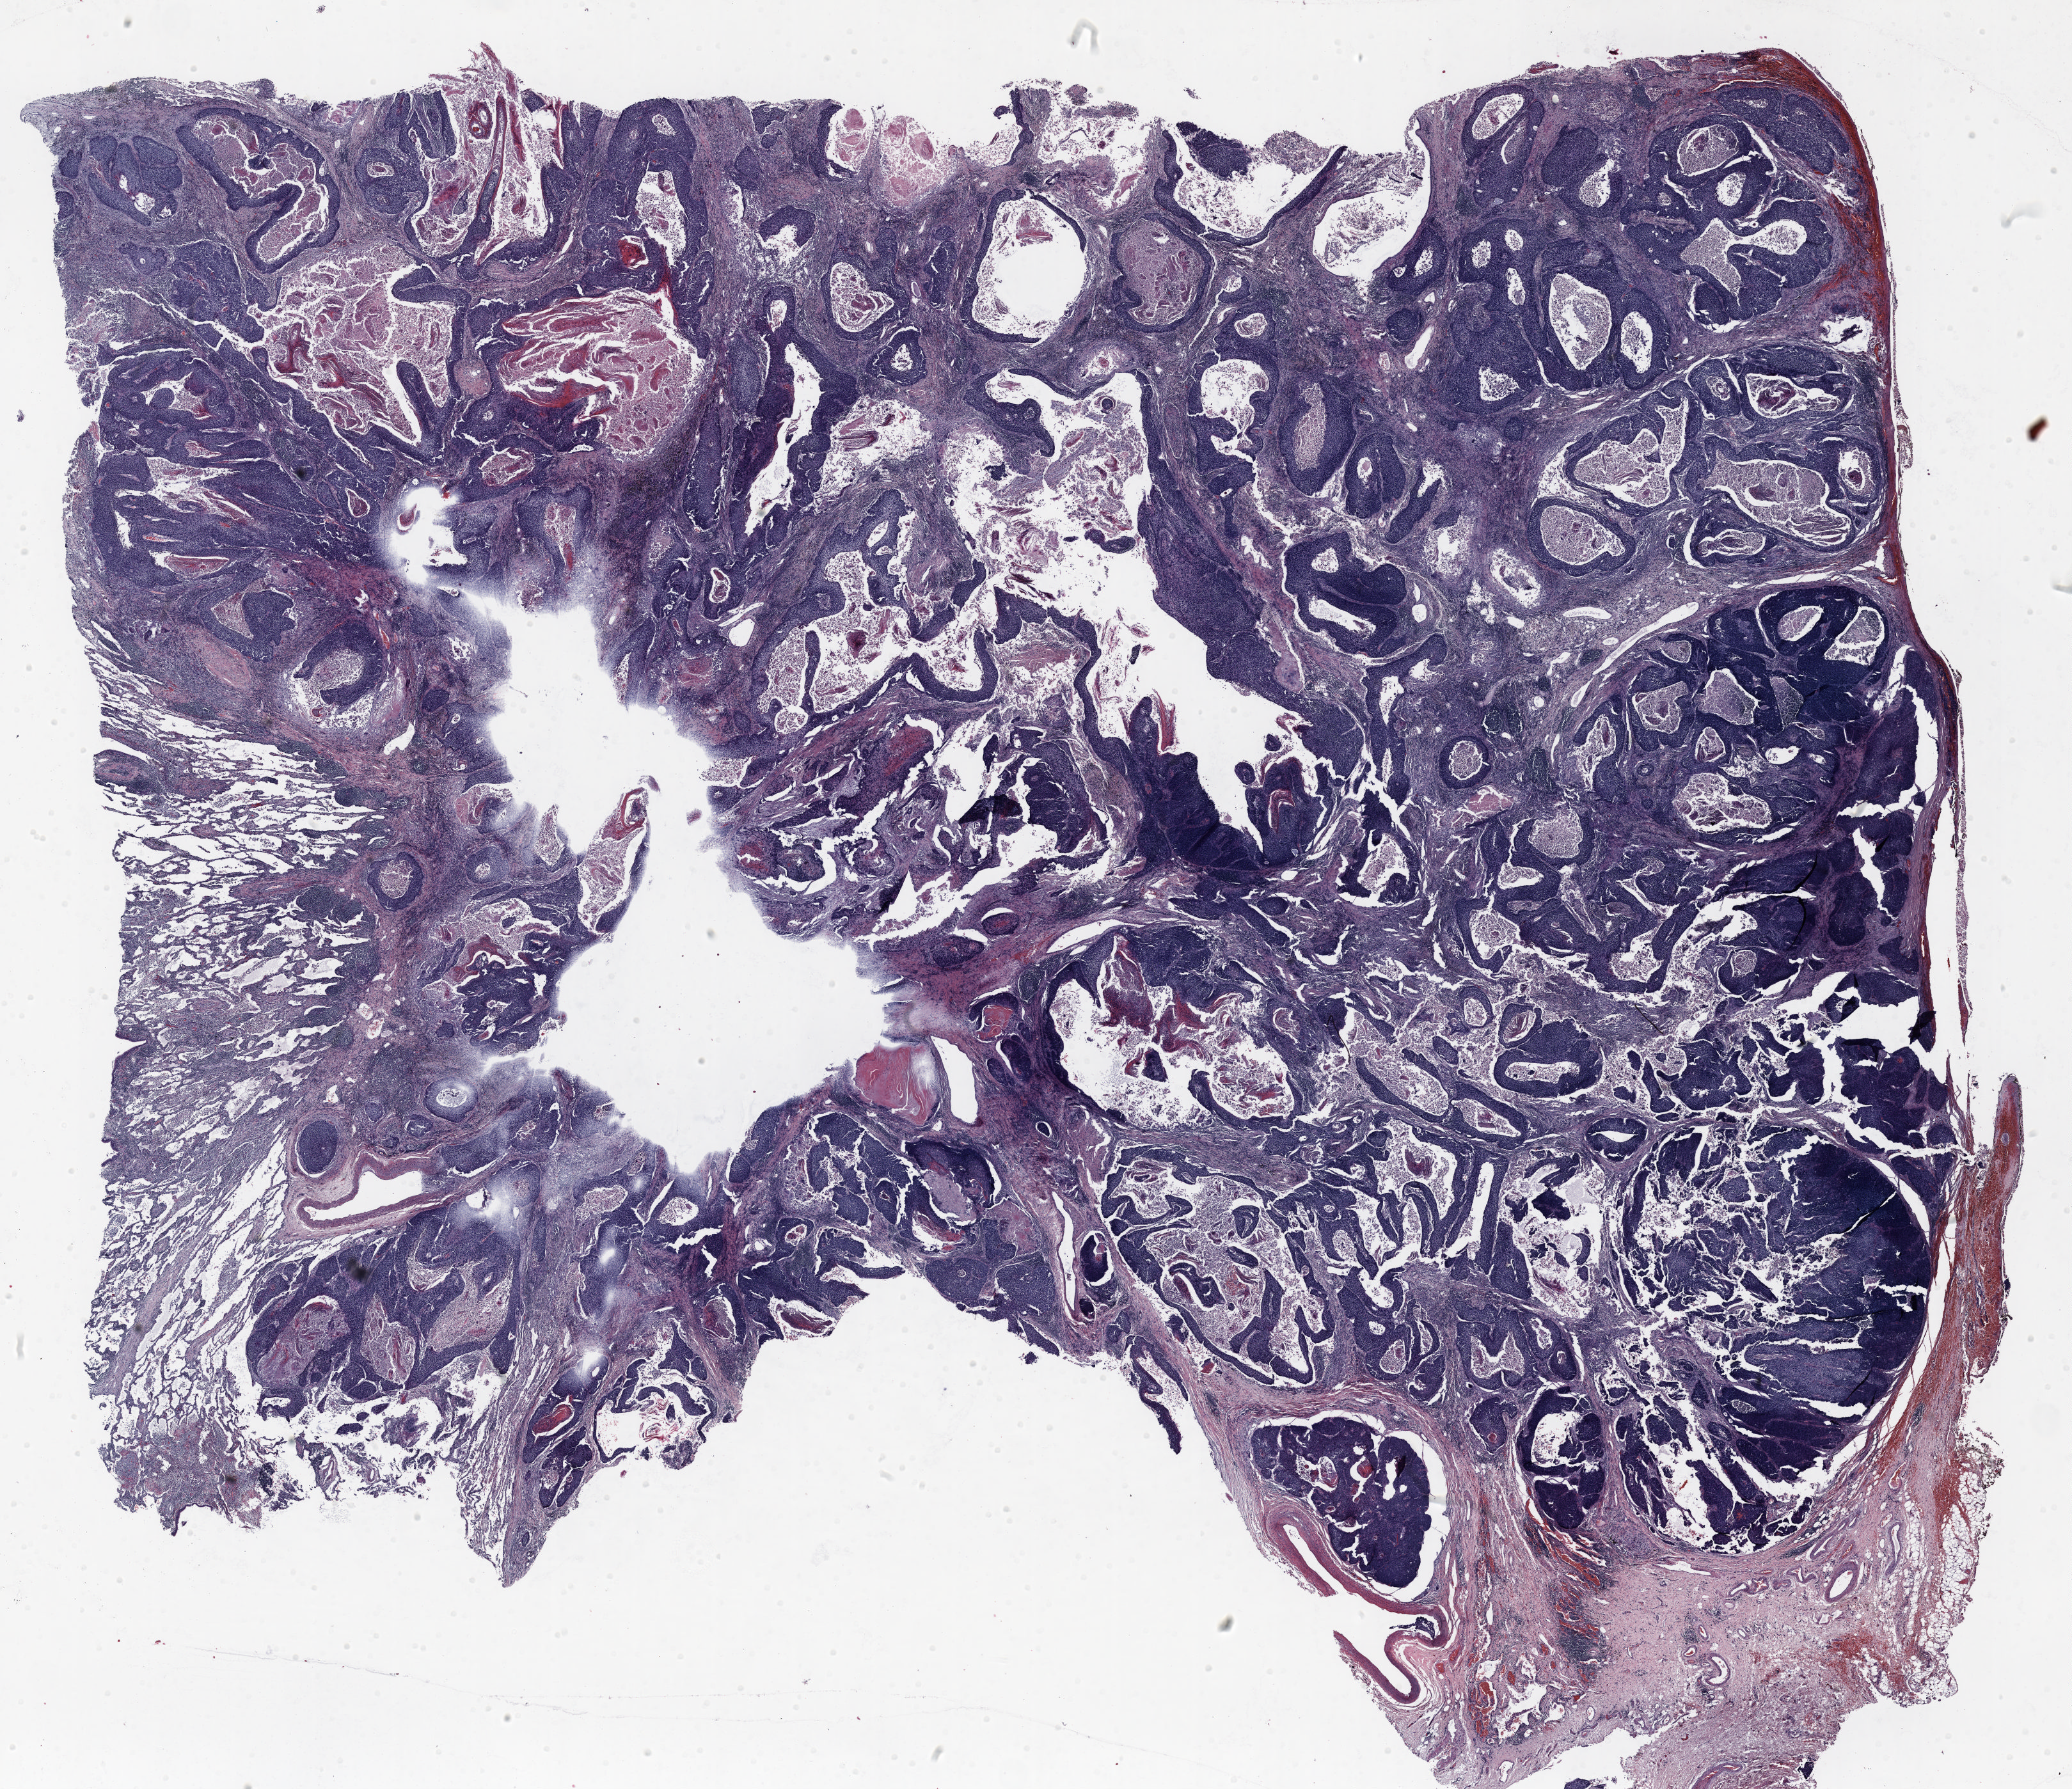
Hematoxylin and eosin (H&E) stained whole-slide image, shown as a low-resolution overview of the whole scanned area (about 26.0 x 22.5 mm, from a 20x scan). FFPE section. Lung. Male, age 70 at enrolment. Current smoker at enrolment.
Participant's lung-cancer diagnosis: Squamous cell carcinoma, NOS (ICD-O-3 8070/3).